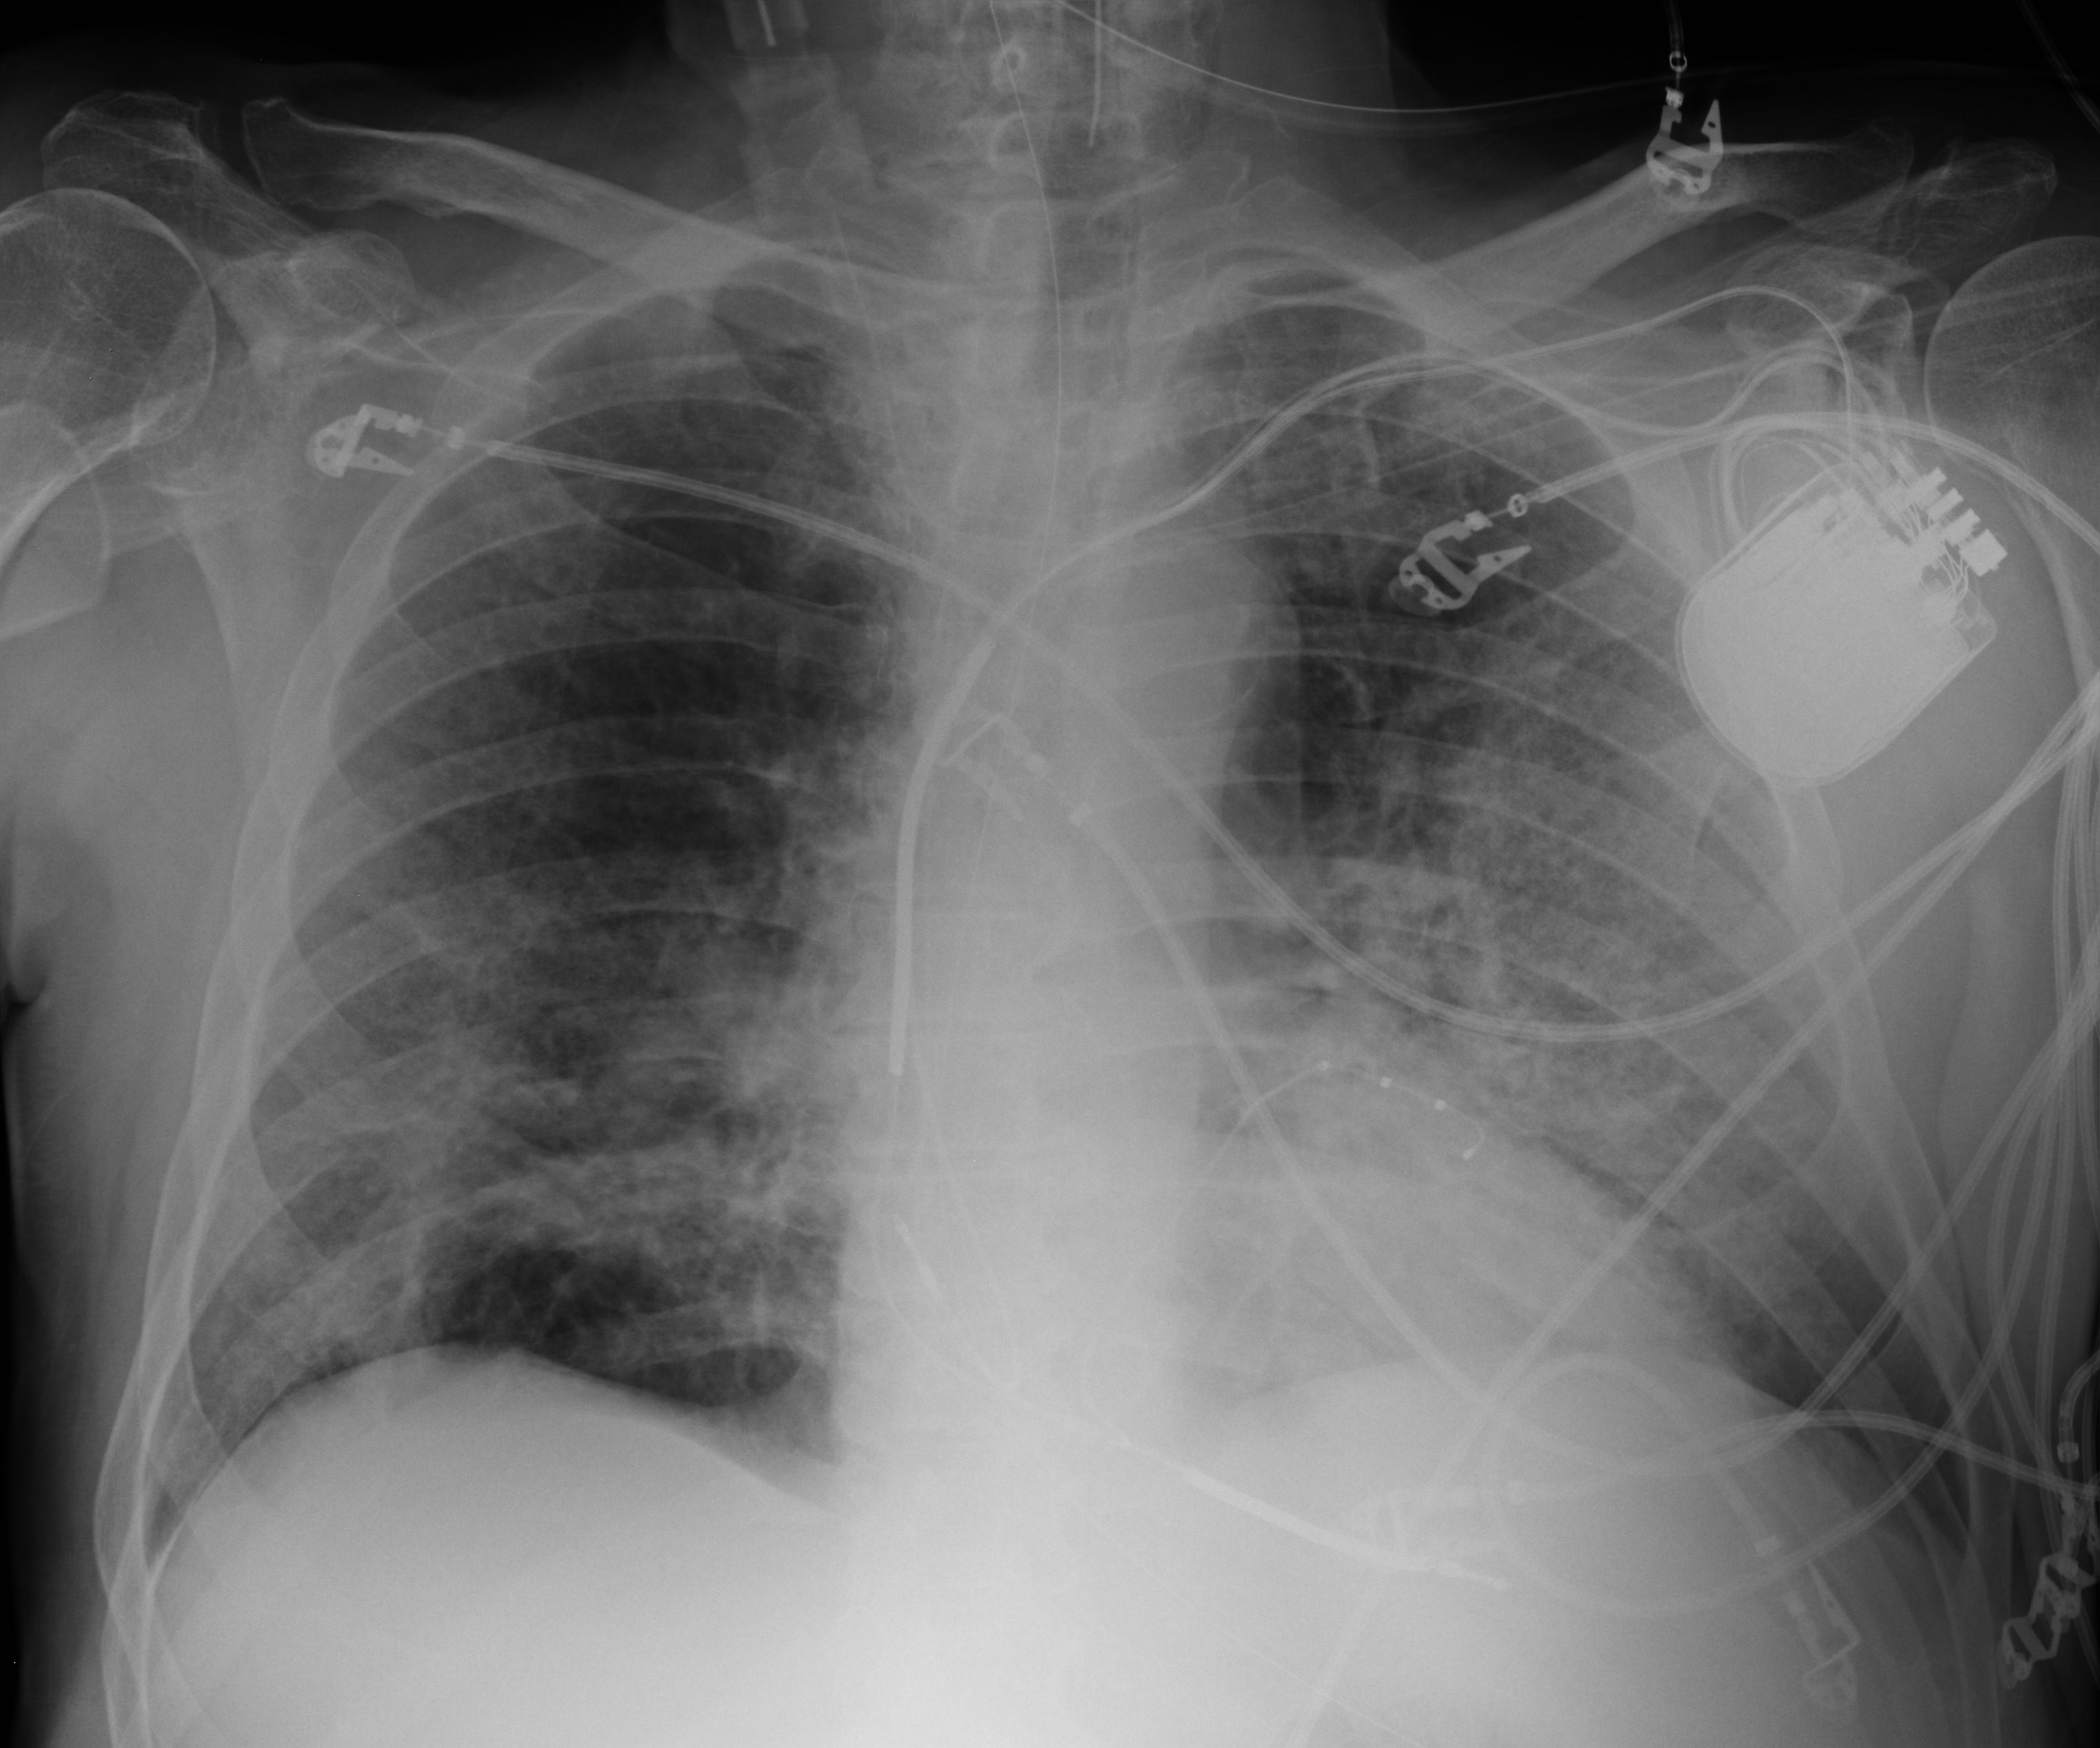
Chest X-ray (portable), anteroposterior (AP) projection. Male patient hospitalised with COVID-19, age 60–74 years.
From the hospital-stay record, not from the radiograph (when in the stay this image was taken is not recorded):
- chronic kidney disease (admission record): no
- length of hospital stay: 36 days